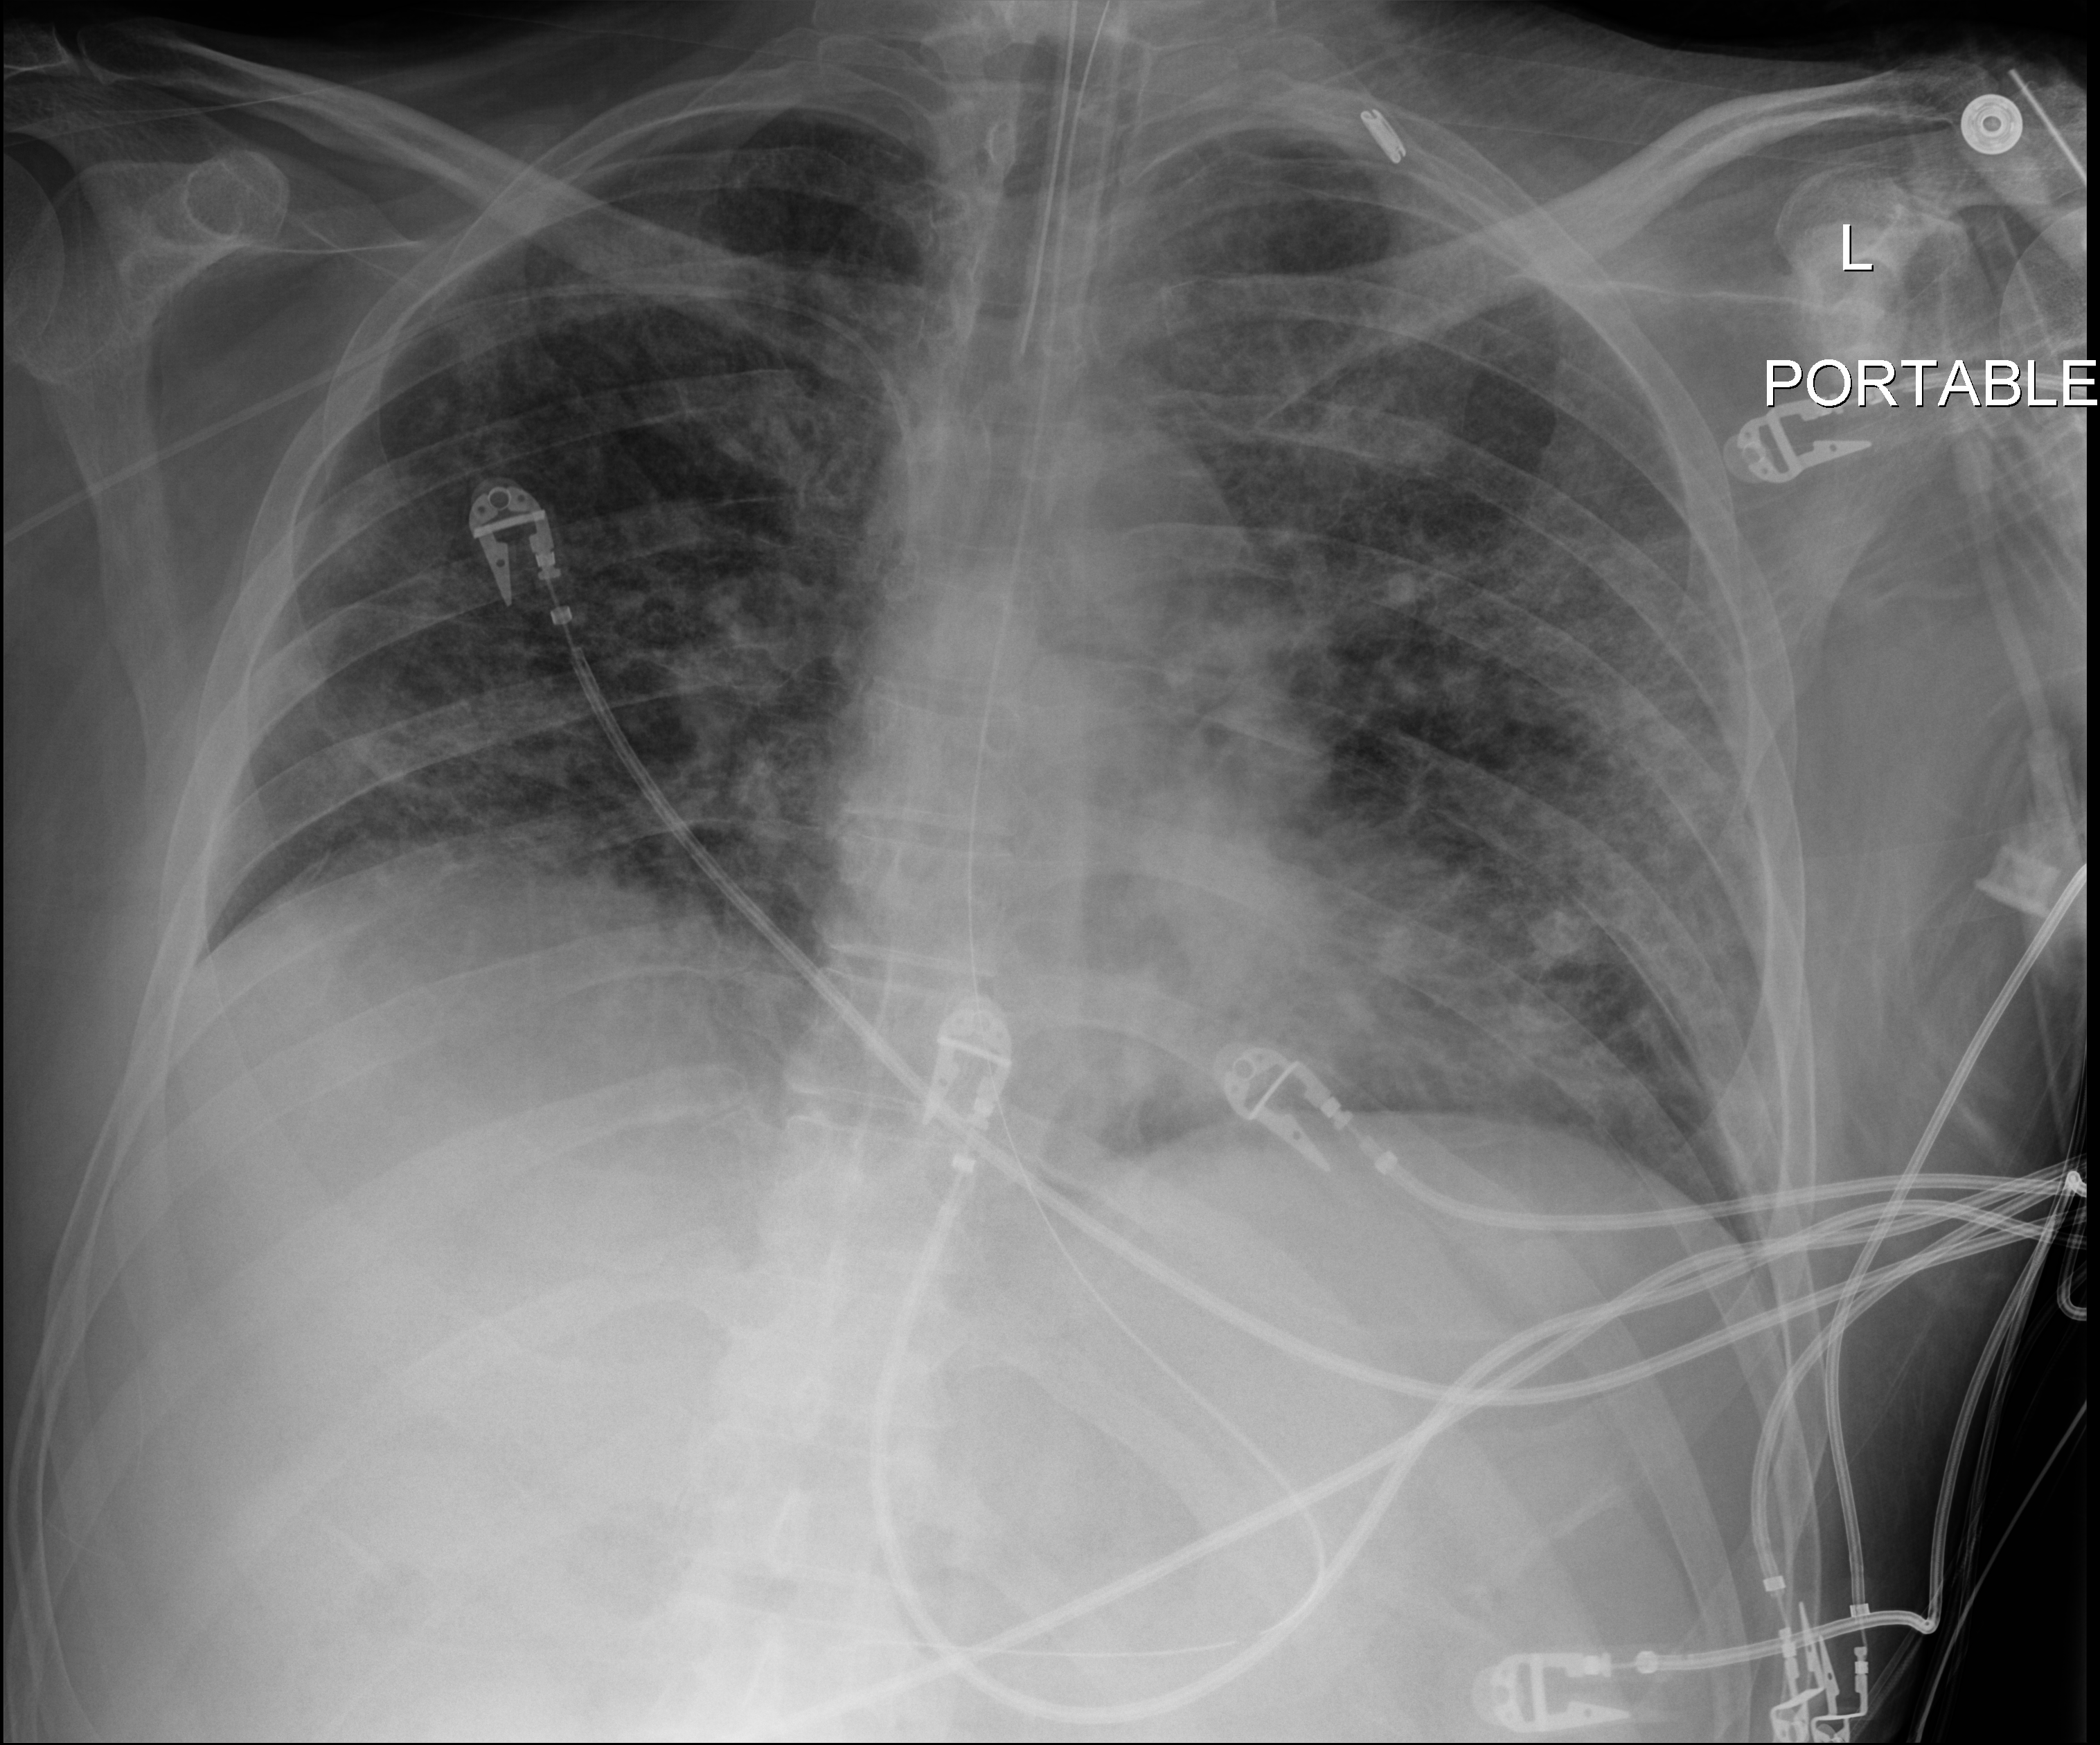
Portable chest radiograph, anteroposterior (AP) projection. Patient hospitalised with COVID-19; male, aged 18–59 years.
From the hospital-stay record, not from the radiograph (when in the stay this image was taken is not recorded):
- length of hospital stay: 48 days